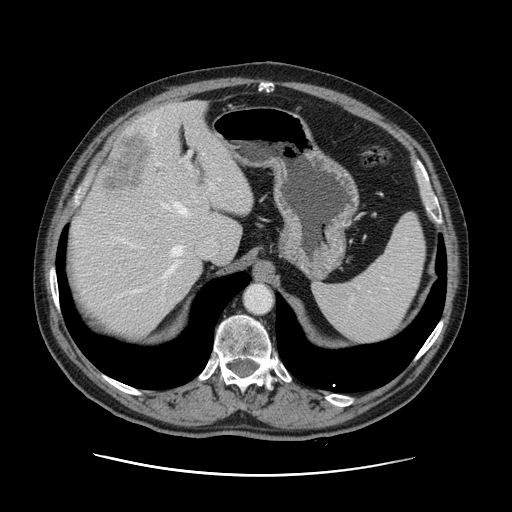
Contrast-enhanced abdominal CT, one axial slice; slice 93 of 141 in the series (ordered by position); 120 kVp; intravenous contrast given; soft-tissue window (W 400 / L 40 HU); 512 × 512 image matrix, field of view 395 × 395 mm. Male patient, age 72 years. Case-level facts recorded for this patient, not image findings: diagnosis: colorectal cancer liver metastases, imaged before liver resection; multiple liver metastases: yes; largest metastasis: 5.4 cm; chemotherapy before resection: yes.
Outlined on this slice (expert manual segmentation):
- hepatic veins: bounding box [x1, y1, x2, y2] px = [132, 153, 204, 293]
- liver: [69, 103, 253, 334]
- planned liver remnant (the part of the liver to remain after resection): [70, 103, 253, 334]
- portal vein (with intrahepatic branches): [116, 151, 215, 241]
- liver metastasis: [100, 130, 155, 197]